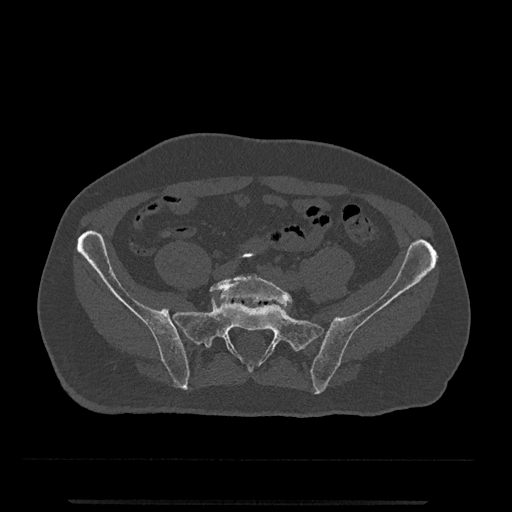
CT including the spine, one axial slice. 120 kVp. Bone window (W 1800 / L 400 HU). 512 × 512 image matrix. Patient: male, 63 years. From the clinical record (not read from this slice): primary cancer: prostate.
Outlined on this slice (semi-automatically segmented with operator editing):
- L5 vertebra: bounding box (x1, y1, x2, y2) in pixels: (210, 274, 292, 308)